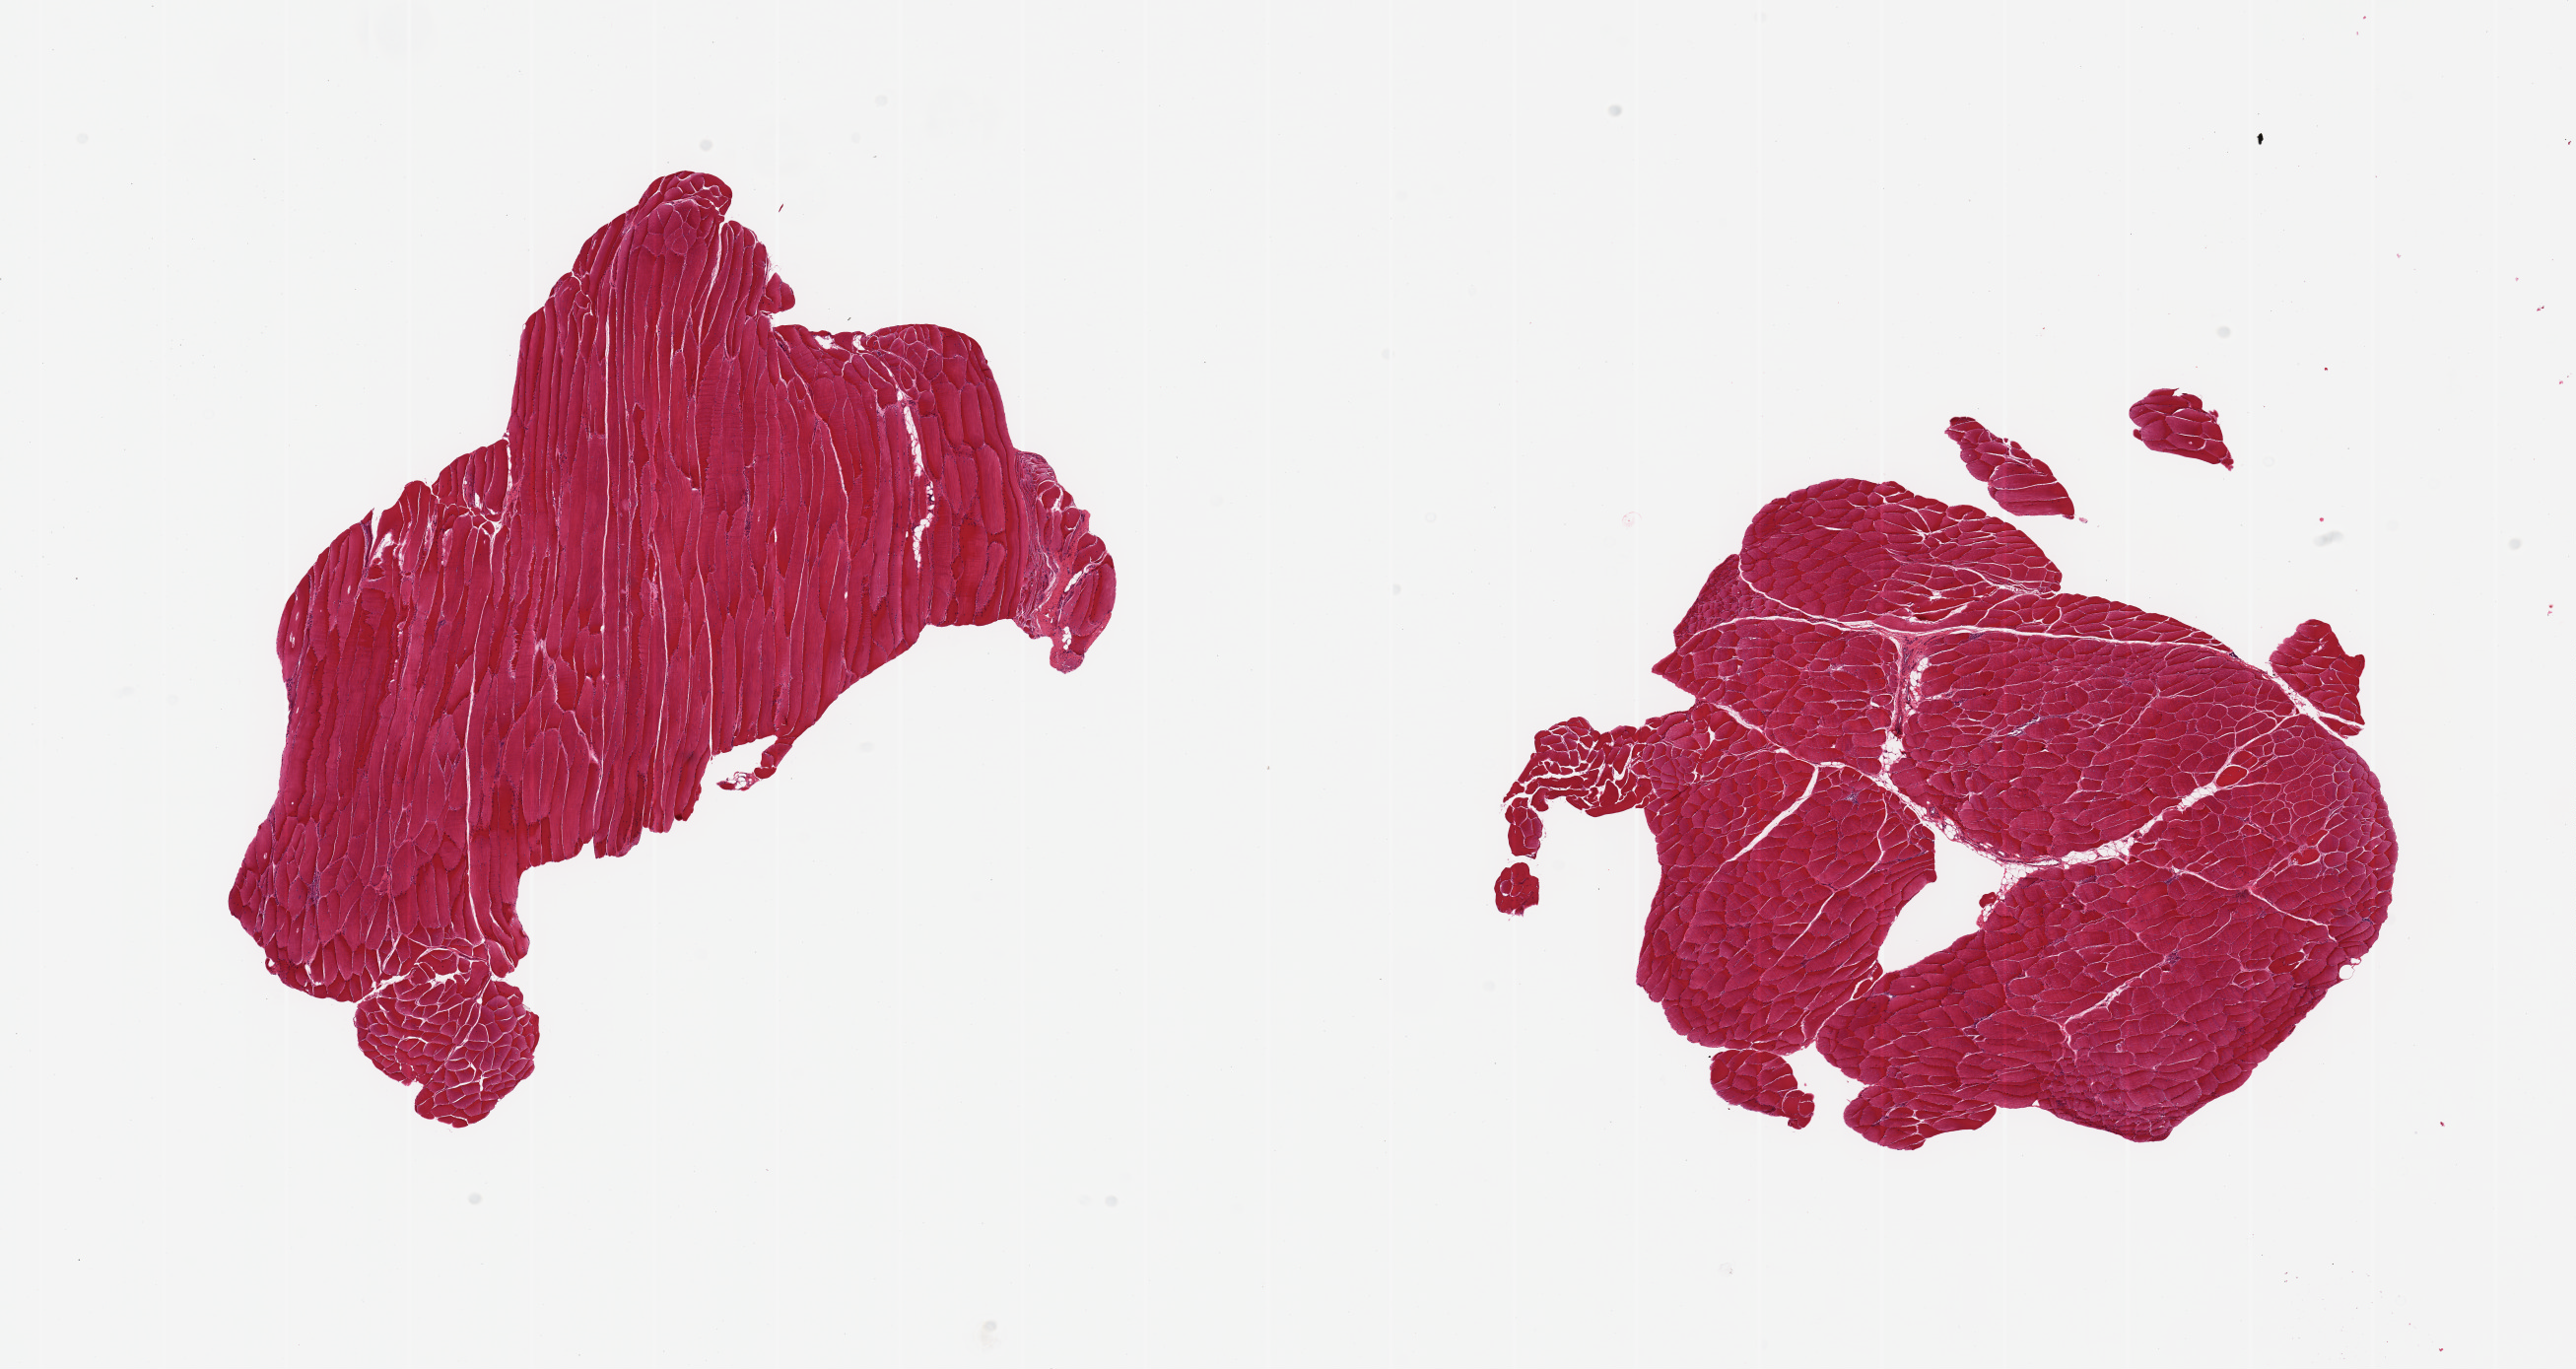
Whole-slide image, H&E stain — whole scanned area (about 20.7 x 11.0 mm, from a 20x scan) shown as a low-resolution overview, PAXgene-fixed, paraffin-embedded tissue, sampled site (target tissue): skeletal muscle, tissue donor sample.
- reviewer comment on this tissue sample: 2 pieces, minimal interstitital fat